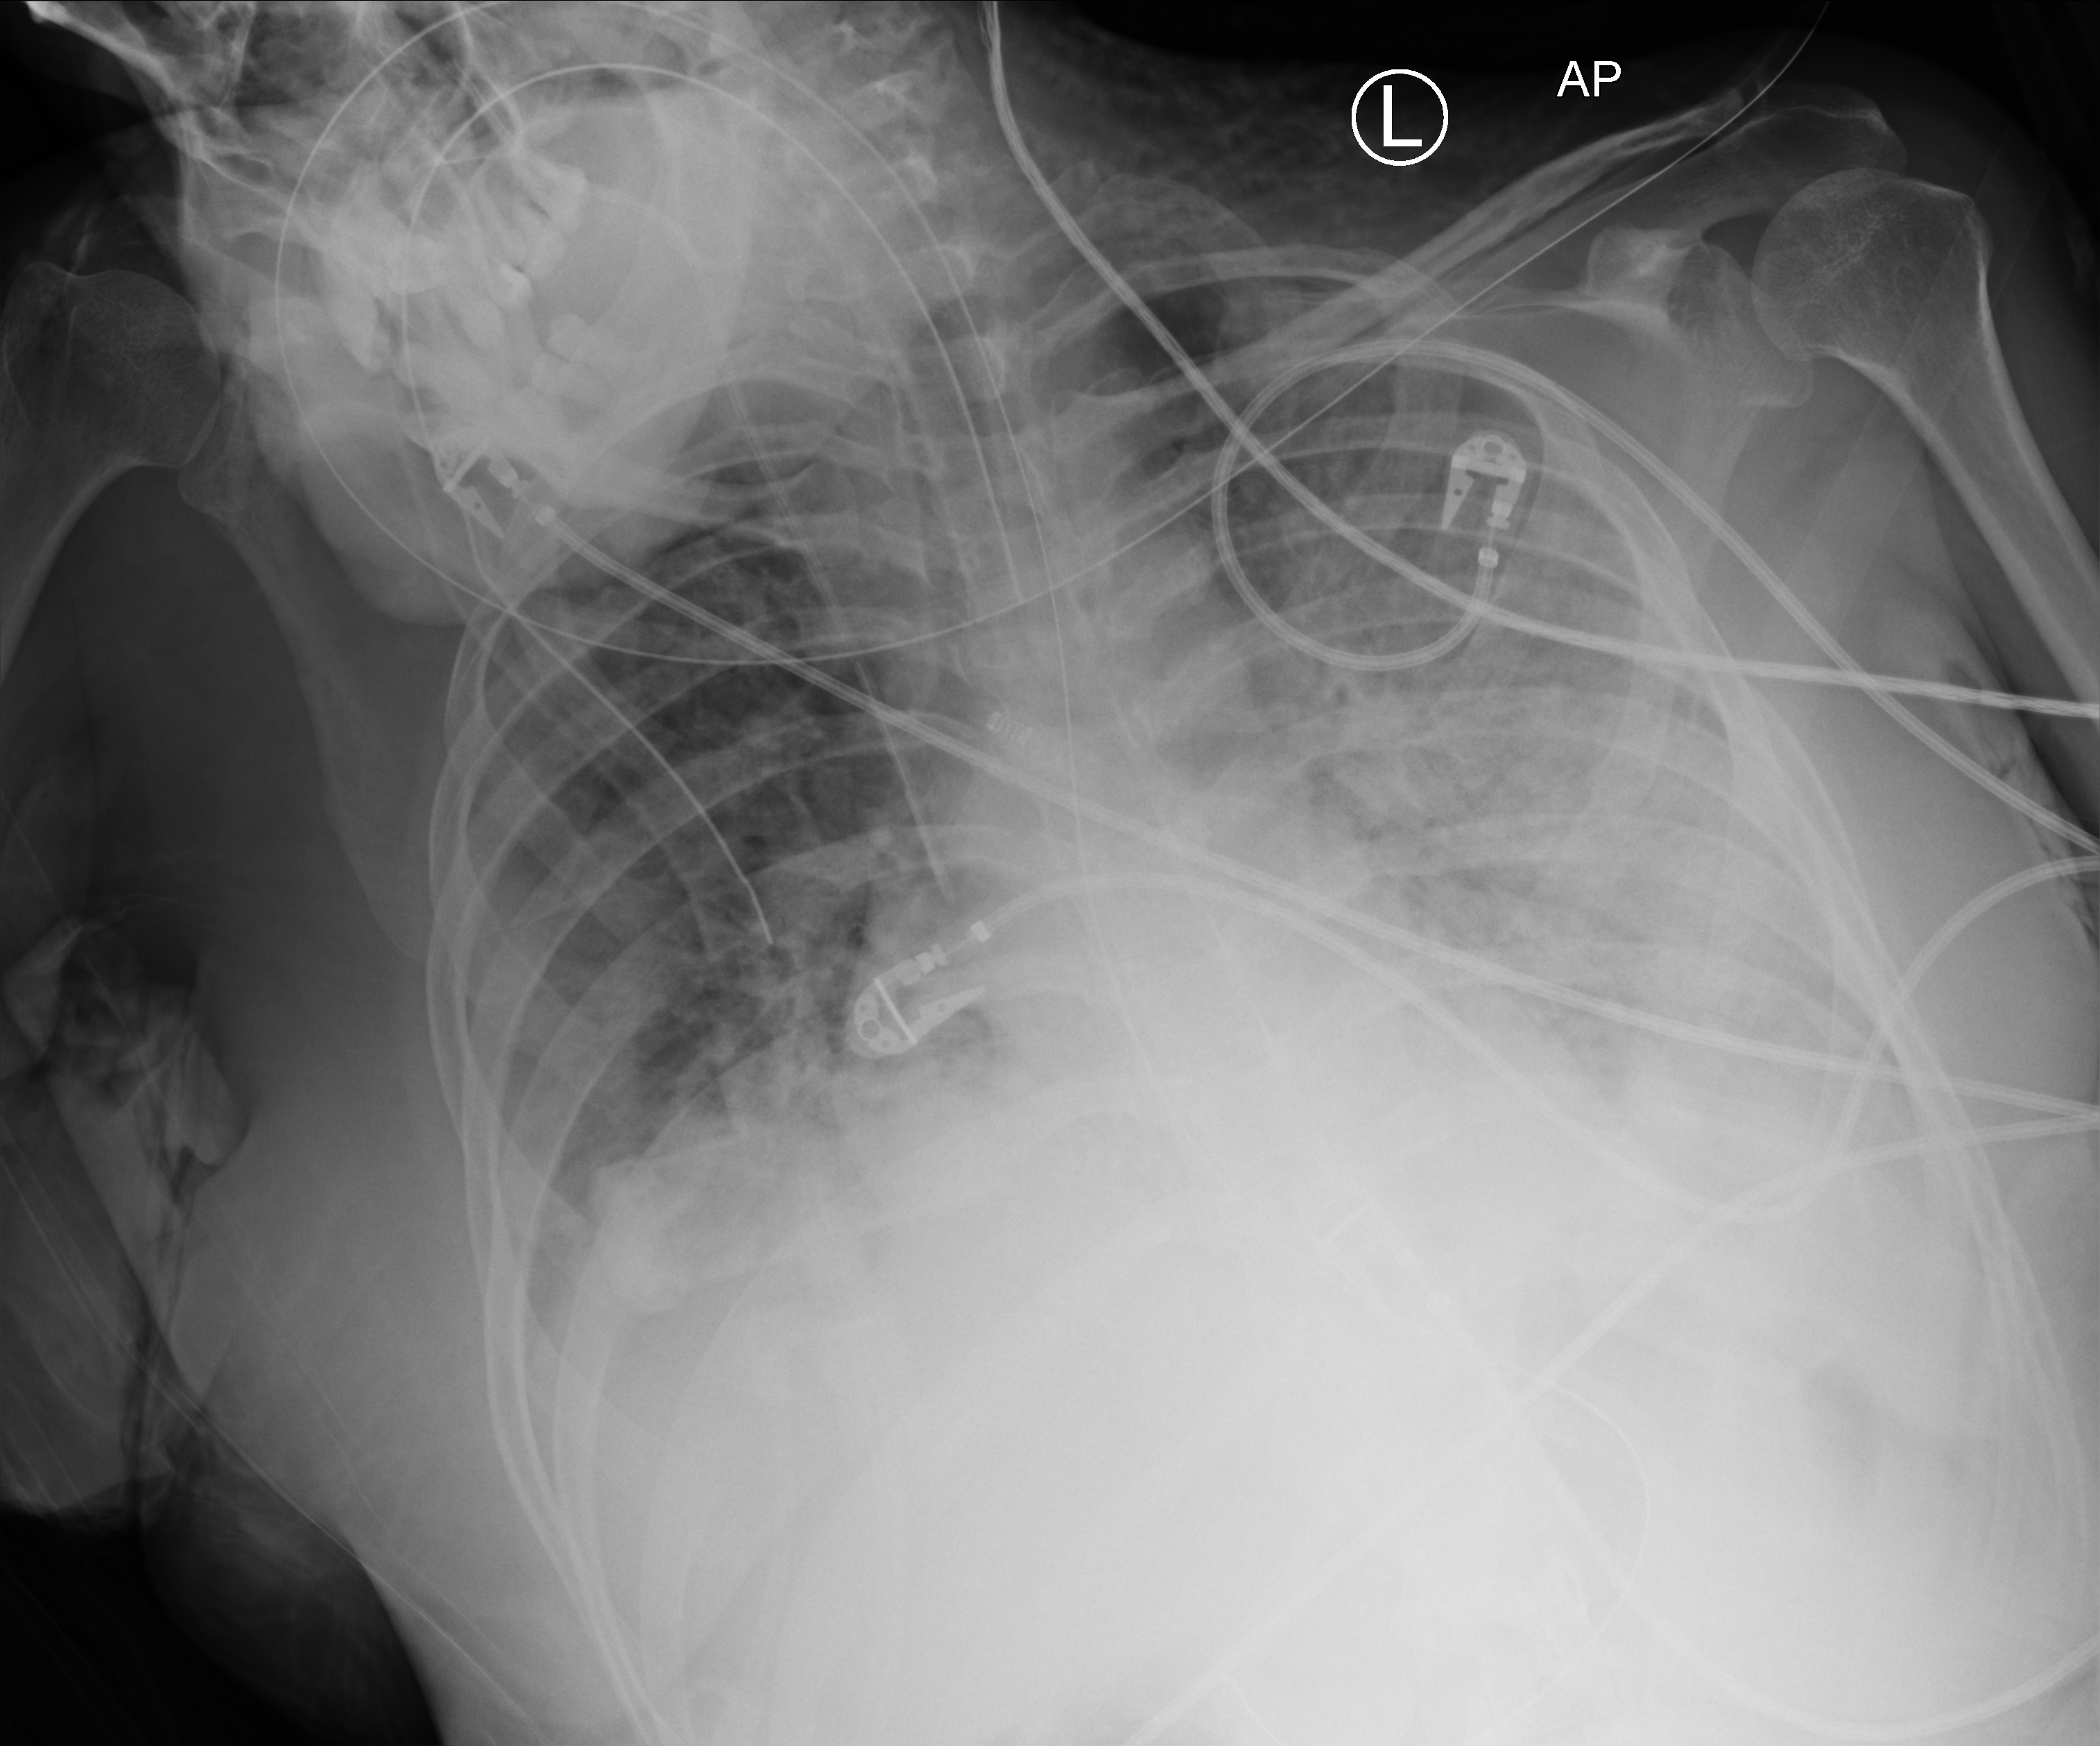
Bedside chest radiograph (computed radiography), anteroposterior (AP) projection. Adult patient hospitalised with COVID-19, age 18–59 years.
Admission-level facts for this patient (not findings on this image; timing relative to this image not recorded): diabetes (admission record): yes.